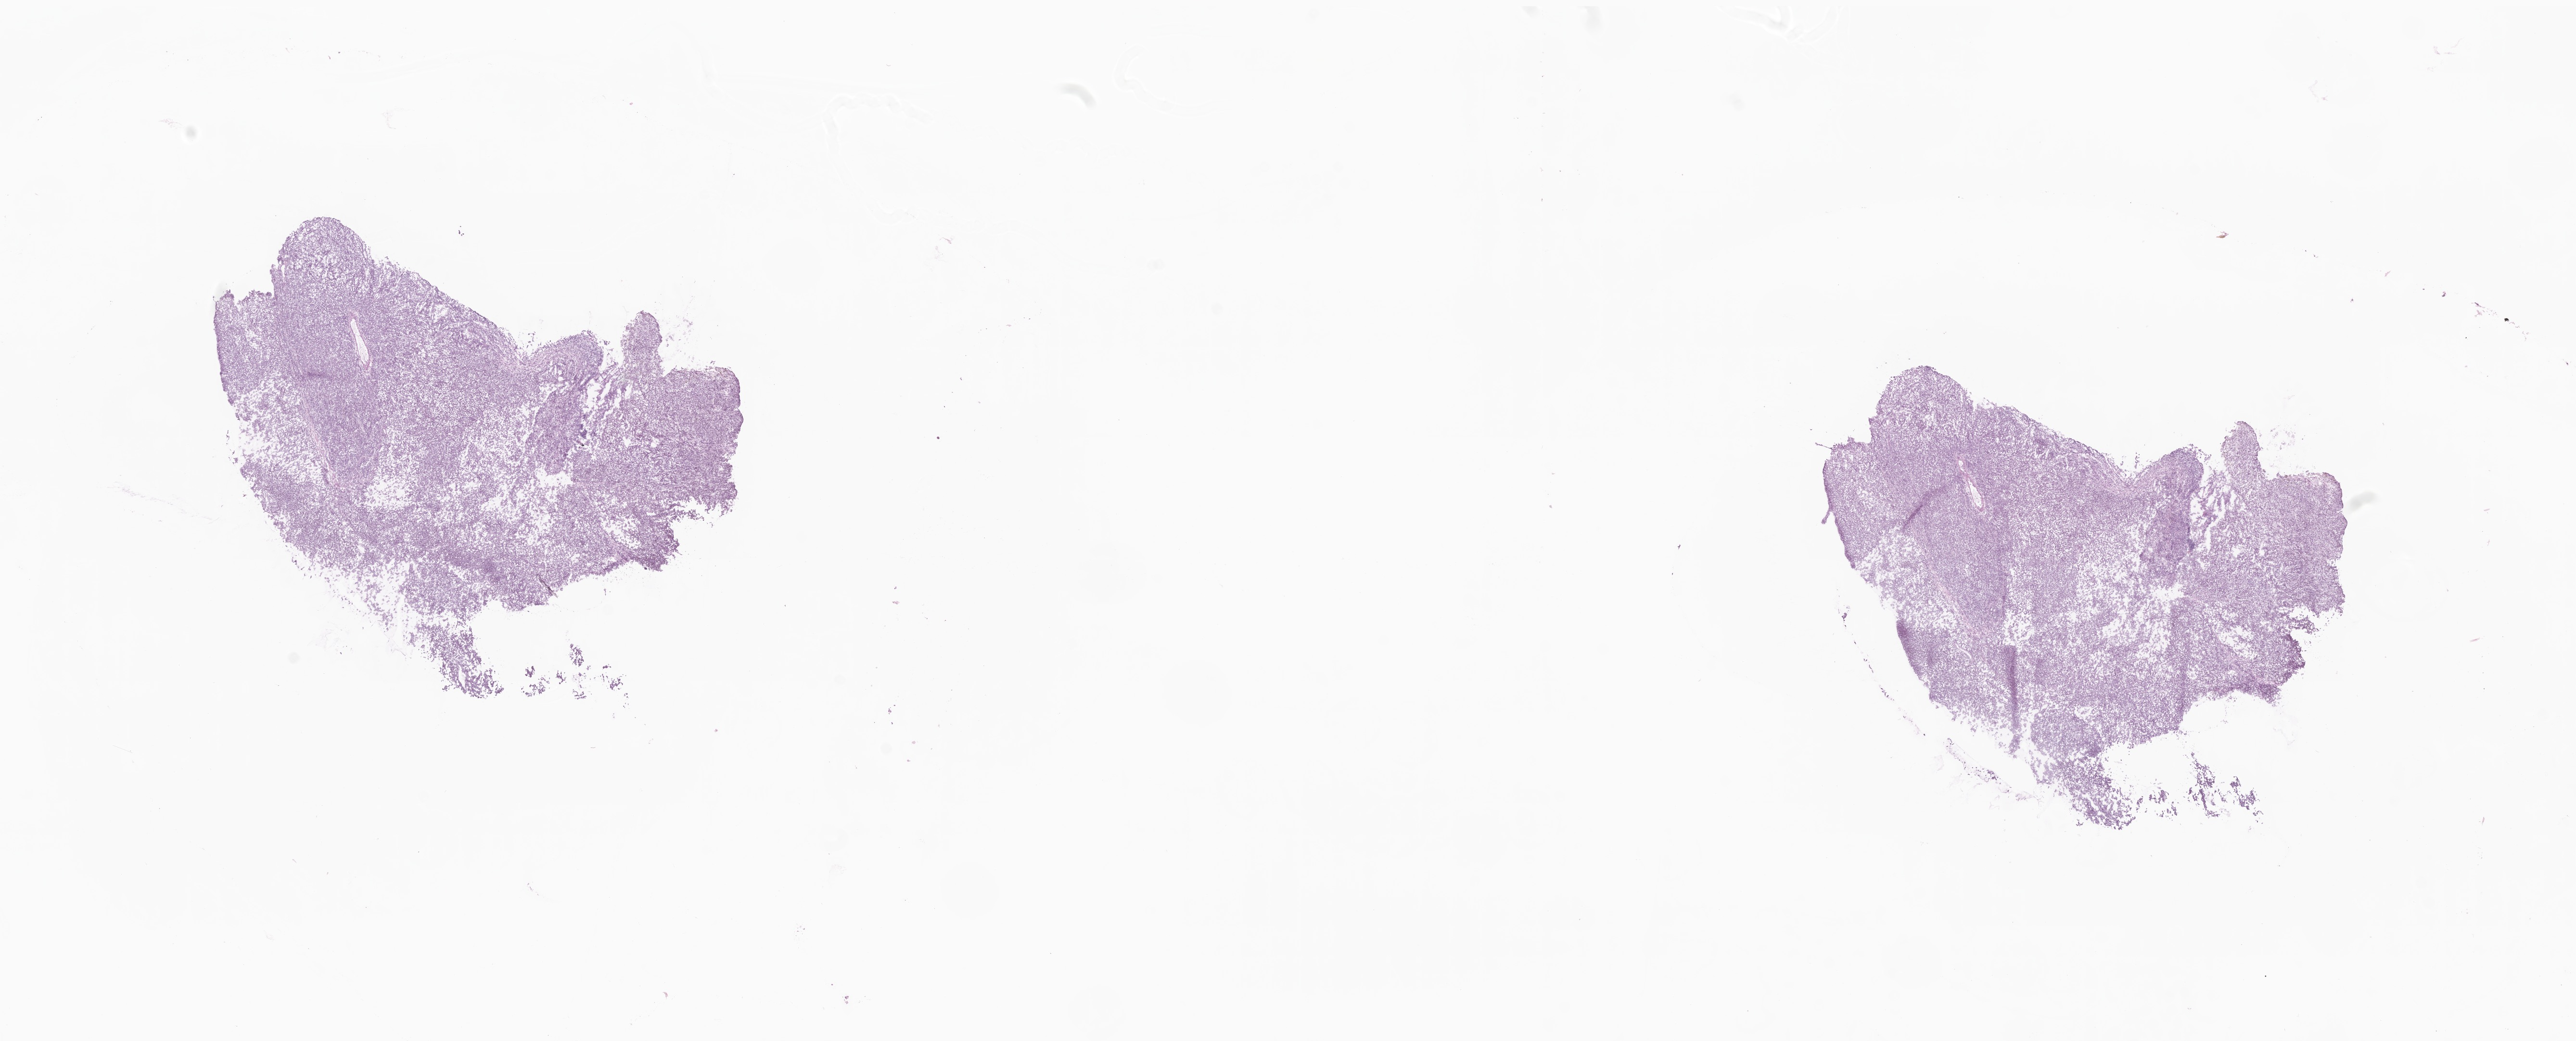
Whole-slide image, hematoxylin and eosin (H&E) stain, whole scanned area (about 22.6 x 9.1 mm) shown as a low-resolution overview. Cryosection. Metastatic tumor tissue, resected from lymph nodes of axilla or arm. Male, age 78 years at initial diagnosis.
Patient diagnosis (primary): Malignant melanoma, NOS.